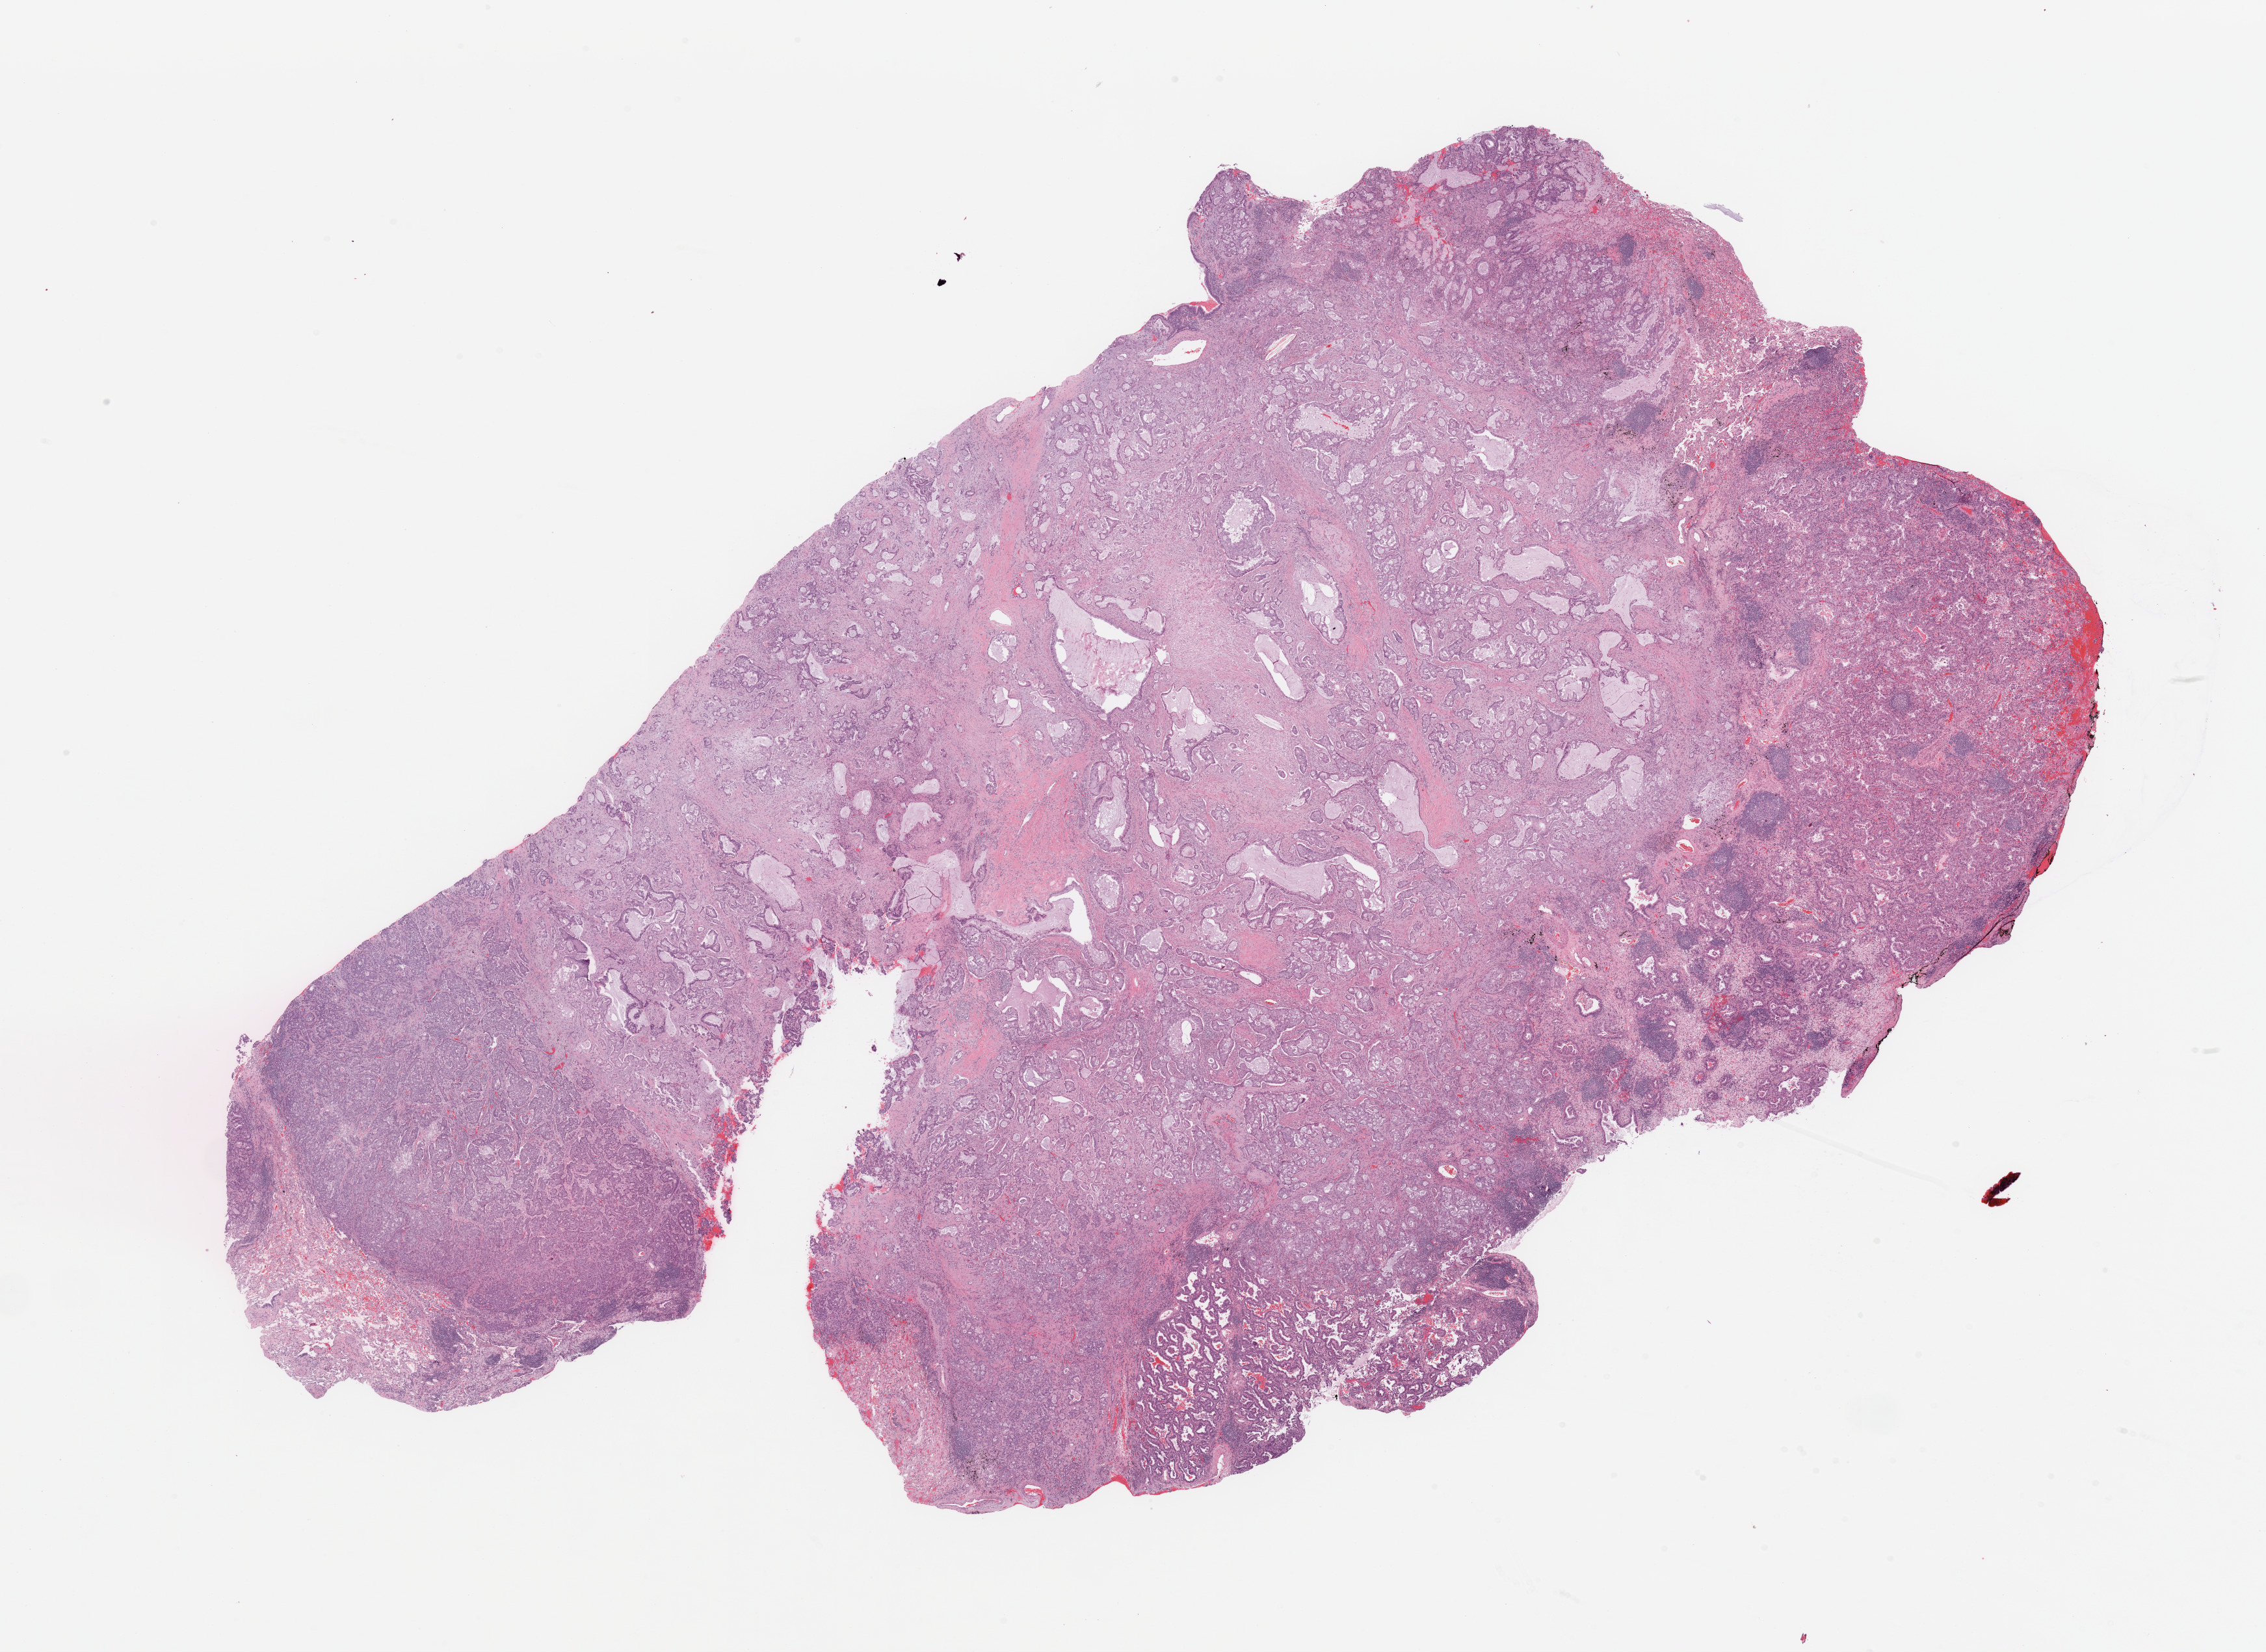
Digitized H&E tissue section (whole slide), a low-resolution overview of the entire scanned area, about 27.6 x 20.1 mm (slide scanned at 20x); tumour tissue sample, sampled site: lung. Patient: female, age 62 years. Pathologist review of this section (percent, as recorded): tumour nuclei 75%, necrosis 5%.
Diagnosis: Adenocarcinoma, NOS.